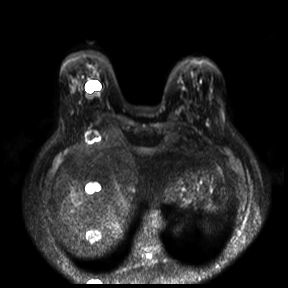
Breast MRI, one axial slice; position 4 of 30 along the scan axis; diffusion-weighted series; image 2 of 4 stored at this slice position (different b-values; order by instance number); 3 T; 288 × 288 image matrix. Female patient.
Annotated regions visible in this slice (manually delineated by an expert):
- tumour on diffusion-weighted imaging: bounding box (x1, y1, x2, y2) in pixels: (206, 121, 209, 124)